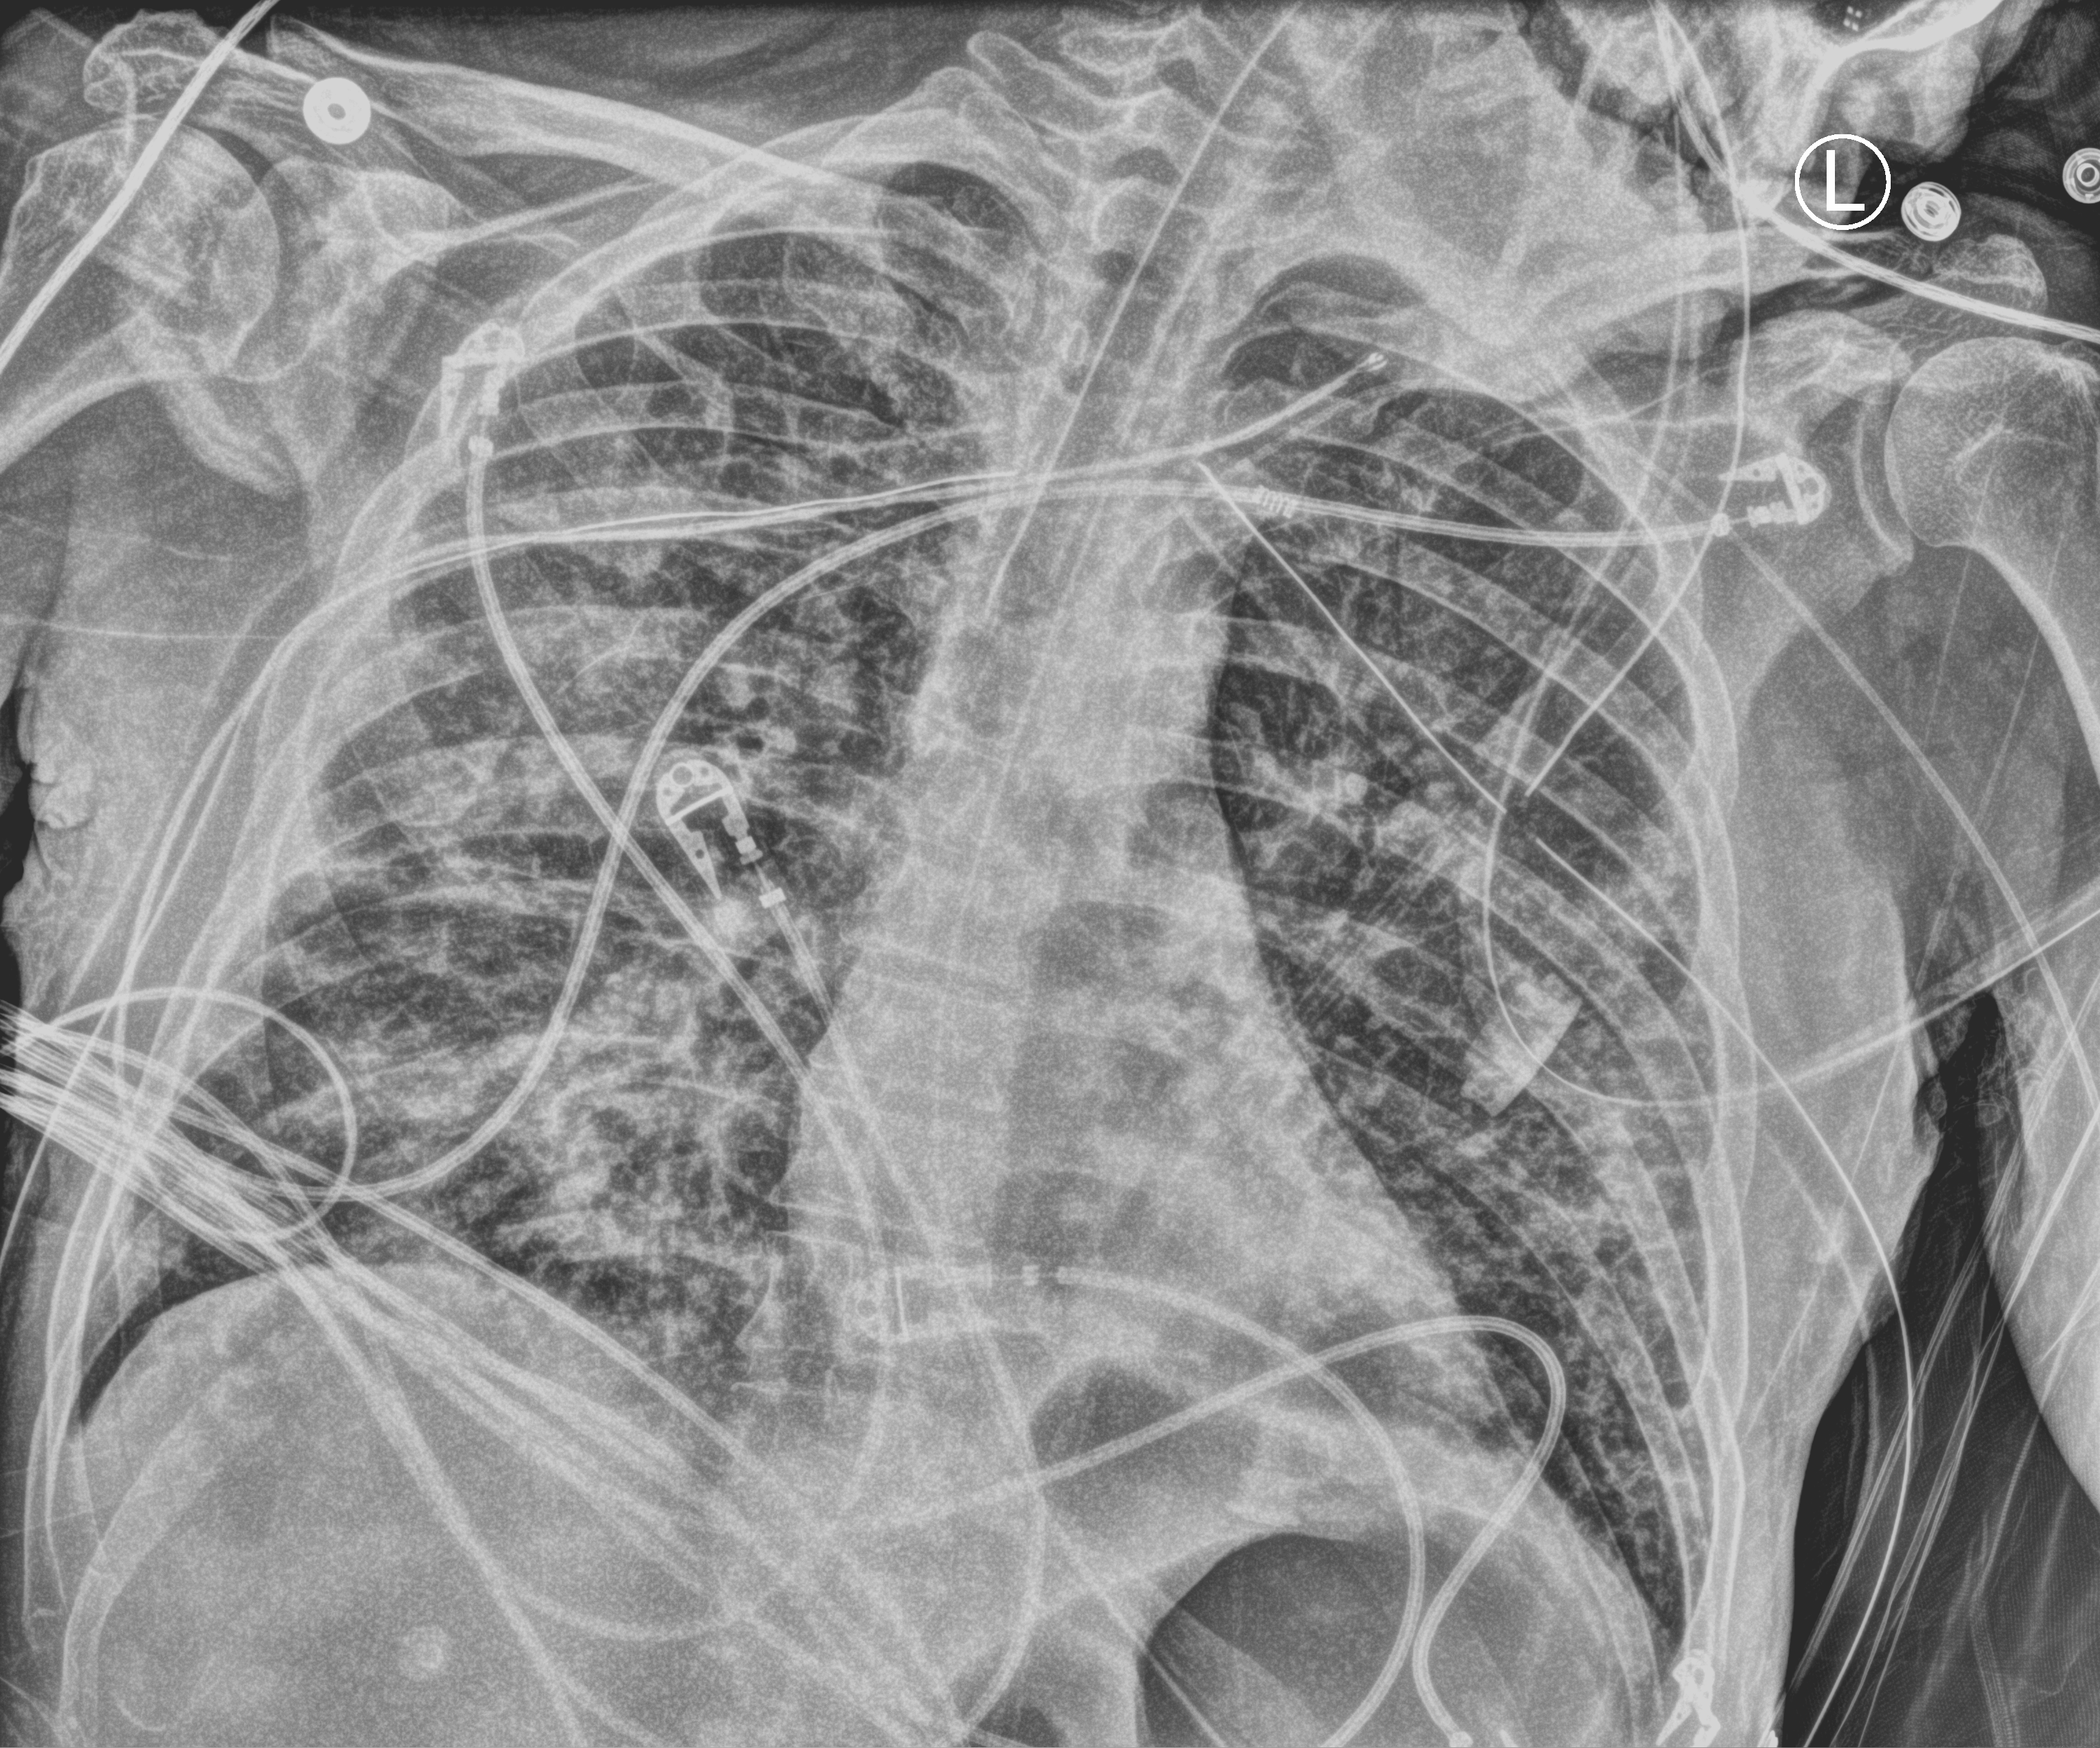
Bedside chest radiograph (computed radiography). Patient hospitalised with COVID-19; male, aged 18–59 years.
Admission-level facts for this patient (not findings on this image; timing relative to this image not recorded):
- length of hospital stay: 96 days
- admitted to intensive care during this hospital stay: yes
- mechanically ventilated during this hospital stay: yes